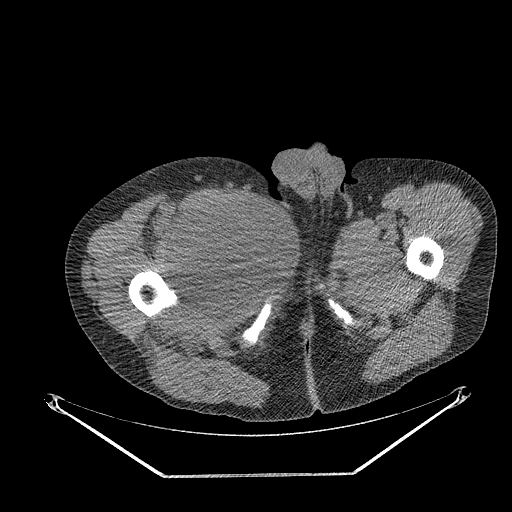
CT of an extremity soft-tissue mass (from a PET/CT study), one axial slice. Slice 282 of 311 in the series (ordered by position). Reconstruction kernel STANDARD. 140 kVp. Soft-tissue window (W 400 / L 40 HU). 3.75 mm slice thickness. 512 × 512 image matrix, field of view 500 × 500 mm. Male patient. From the clinical record (not read from this slice): histological type: undifferentiated - pleiomorphic; grade: high; site of the primary tumour: right thigh.
Structures marked on this image (expert contour drawn on MRI and transferred to this co-registered scan by the dataset authors):
- gross tumour volume including surrounding oedema: bounding box <180,192,259,277> (left, top, right, bottom; pixels)
- gross tumour volume (mass): <180,199,259,275>